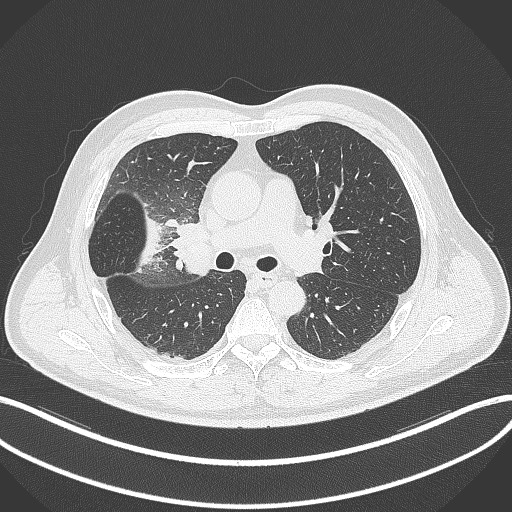
Chest CT, one axial slice. Slice 198 of 348 in the series (ordered by position). Reconstruction kernel B70f. Lung window (W 1500 / L -600 HU). 1 mm slice thickness. 512 × 512 image matrix. Patient: male, 55 years. Case-level facts recorded for this patient, not image findings: clinical TNM (as recorded): T3 N2 M1.
Outlined on this slice (rectangle marked by the reading radiologist):
- lung tumour (recorded histology: adenocarcinoma): box from (x=138, y=208) to (x=165, y=274) px